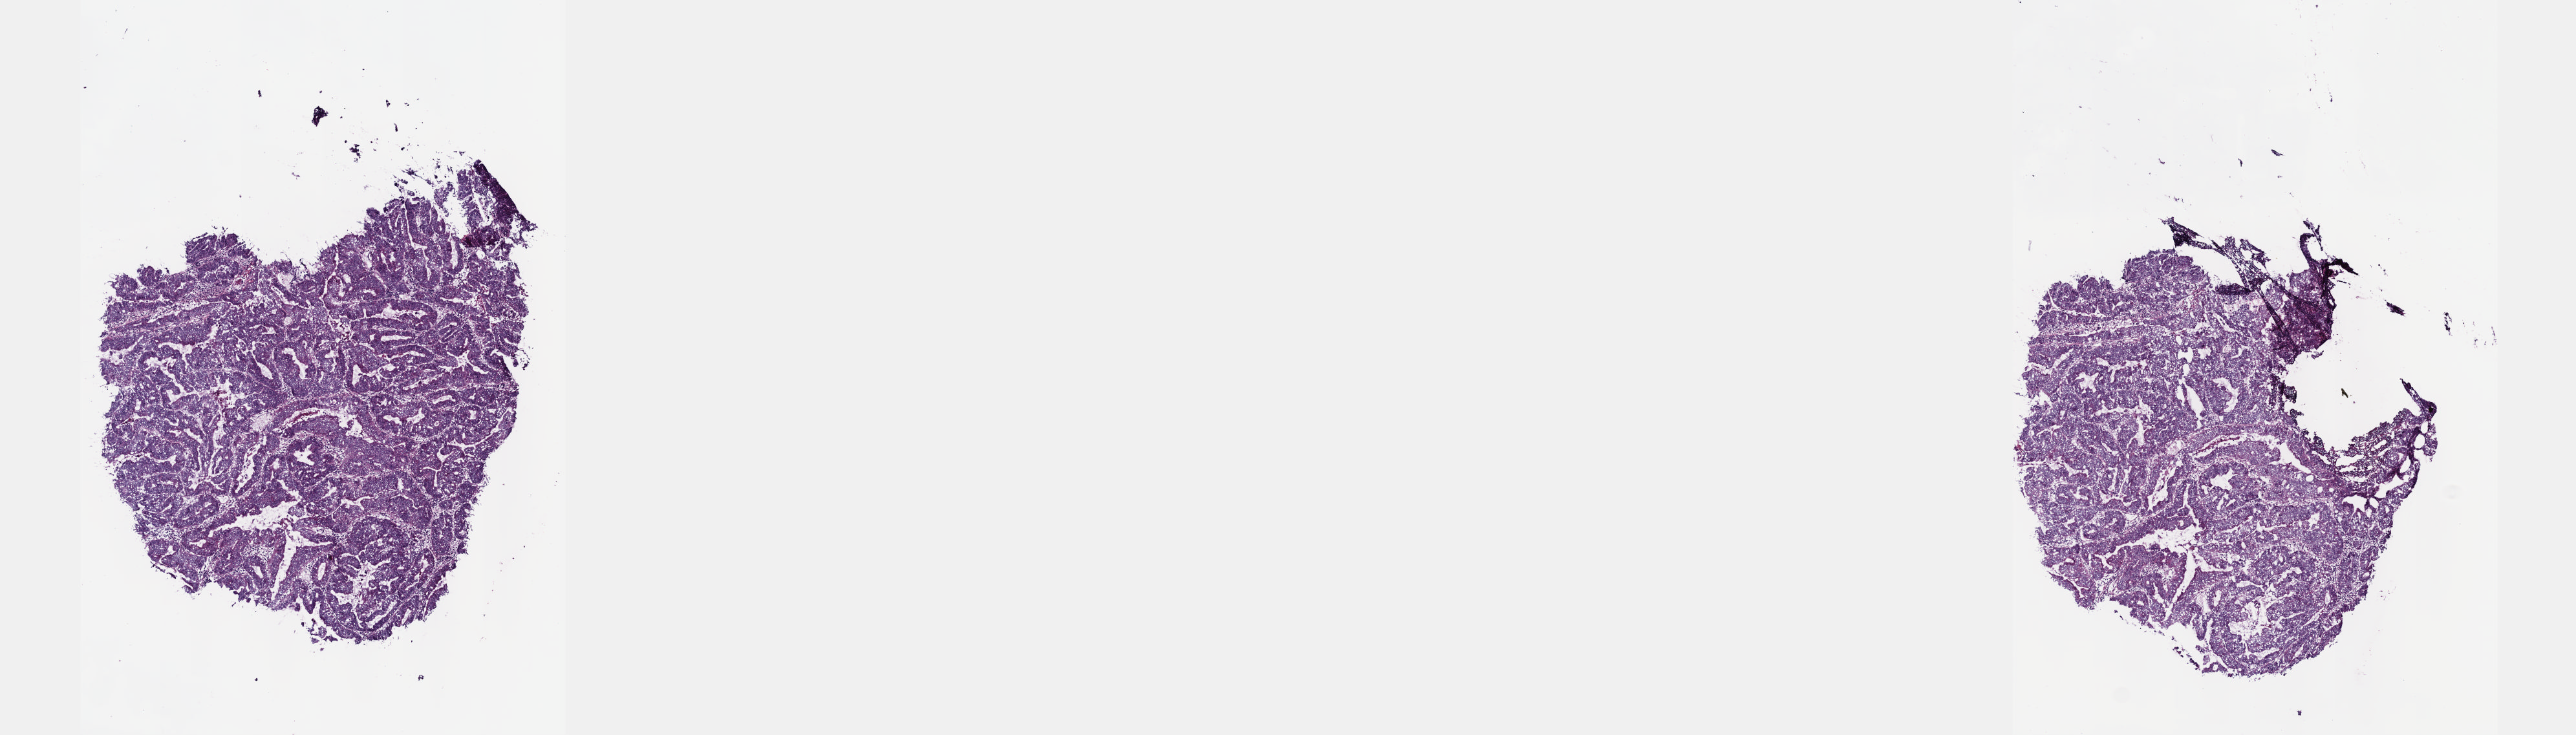
Digitized H&E-stained tissue section (whole slide) — shown as a low-resolution overview of the whole scanned area (about 16.1 x 4.6 mm, from a 40x scan), frozen section from the top of the tissue portion, primary tumour sample from the esophagus. Patient: male, age at initial diagnosis 77 years. Histologic grade: GX (grade cannot be assessed). Pathologist review of this section (percent, as recorded): tumour cells 94%, tumour nuclei 98%, normal cells 0%, stromal cells 5%, necrosis 1%. Inflammatory infiltration, as recorded: lymphocyte infiltration 2%, monocyte infiltration 3%, neutrophil infiltration 1%.
* diagnosis: Adenocarcinoma, NOS
* AJCC pathologic stage: IIB (5th edition)
* lymph nodes positive (case pathology): 1 of 12 examined
* TNM: T2 N1 M0